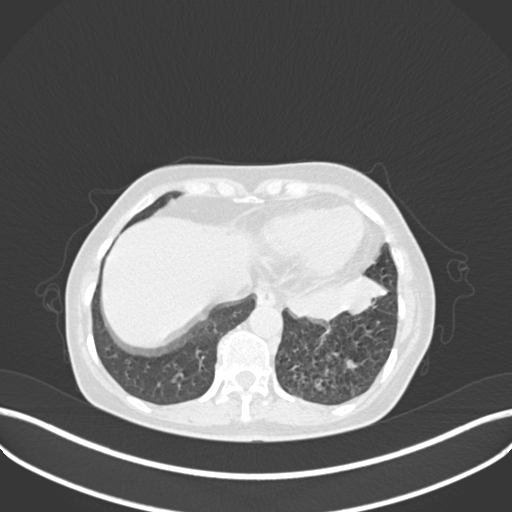
Chest CT, one axial slice. Slice 56 of 270 in the series (ordered by position). Reconstruction kernel B30f. 120 kVp. Lung window (W 1500 / L -600 HU). 512 × 512 image matrix, field of view 400 × 400 mm. Female patient, age 63 years. Case-level facts recorded for this patient, not image findings: clinical TNM (as recorded): T1b N0 M0.
Outlined on this slice (bounding box drawn by a radiologist):
- lung tumour (recorded histology: adenocarcinoma): bounding box (x1, y1, x2, y2) in pixels: (278, 274, 391, 327)